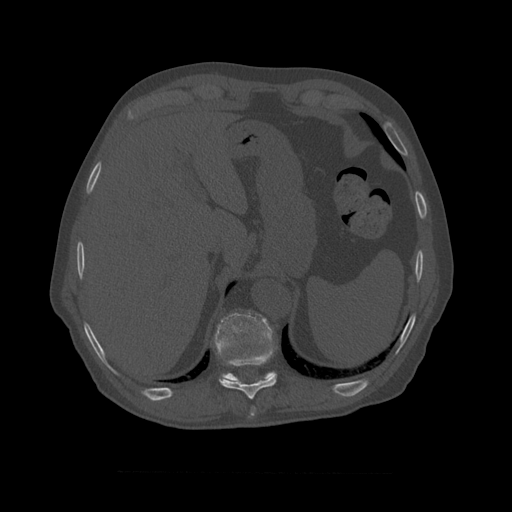
CT including the spine, one axial slice. Slice 417 of 450 in the series (ordered by position). 120 kVp. Bone window (W 1800 / L 400 HU). 512 × 512 image matrix, field of view 405 × 405 mm. Patient age 75 years. From the clinical record (not read from this slice): primary cancer: prostate.
Outlined on this slice (semi-automatic segmentation, software-assisted and operator-edited):
- T10 vertebra: bounding box <214,311,277,382> (left, top, right, bottom; pixels)
- T8 vertebra: <252,407,256,411>
- T9 vertebra: <218,345,277,410>